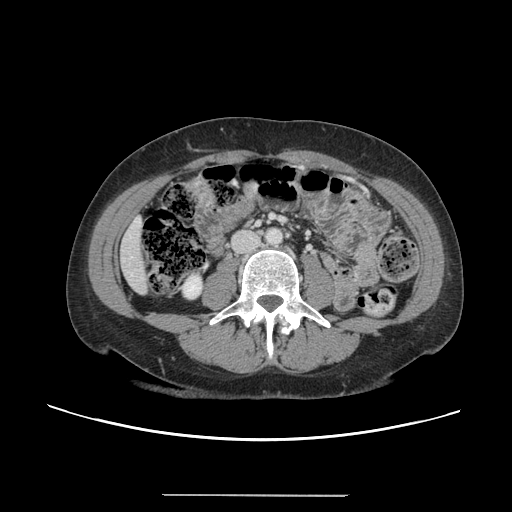
Contrast-enhanced abdominal CT, one axial slice; position 21 of 144 along the scan axis; intravenous contrast given; soft-tissue window (W 400 / L 40 HU); 2.5 mm slice thickness; 512 × 512 image matrix. Female patient, age 53 years. From the clinical record (not read from this slice): diagnosis: colorectal cancer liver metastases, imaged before liver resection; multiple liver metastases: yes; largest metastasis: 1.1 cm; disease in both lobes: no.
Annotated regions visible in this slice (manually delineated by an expert):
- liver: box from (x=120, y=218) to (x=148, y=294) px
- planned liver remnant (the part of the liver to remain after resection): (x=120, y=218)–(x=148, y=295)